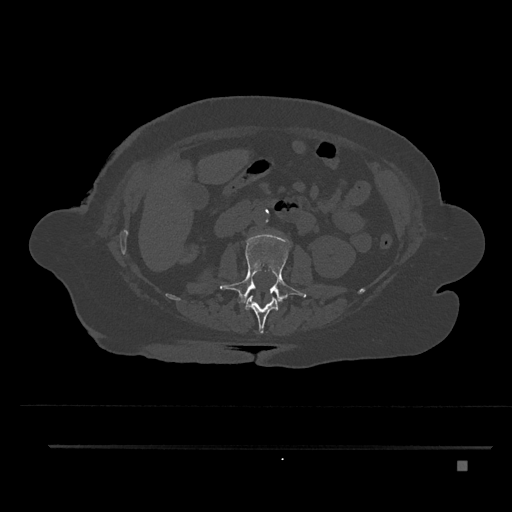
CT including the spine, one axial slice; position 182 of 797 along the scan axis; bone window (W 1800 / L 400 HU); 0.5 mm slice thickness; 512 × 512 image matrix, field of view 437 × 437 mm. Patient: female, 76 years. Case-level facts recorded for this patient, not image findings: primary cancer: lung; vertebrae with lytic lesions (as recorded): T11, L3.
Structures marked on this image (semi-automatically segmented with operator editing):
- L1 vertebra: box from (x=245, y=296) to (x=279, y=333) px
- L2 vertebra: (x=220, y=234)–(x=306, y=304)